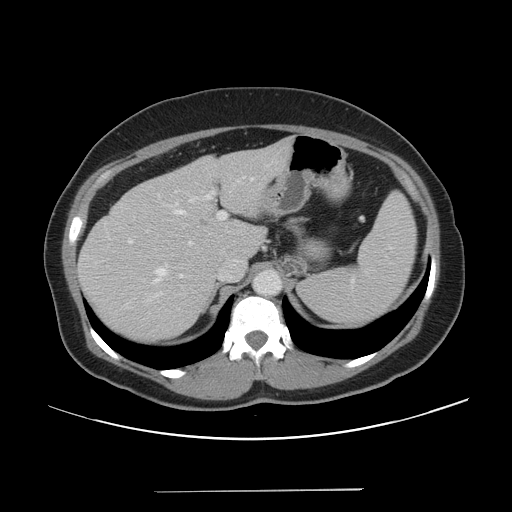
Contrast-enhanced abdominal CT, one axial slice; slice 31 of 56 in the series (ordered by position); 120 kVp; intravenous contrast given; soft-tissue window (W 400 / L 40 HU); 512 × 512 image matrix. Female patient, age 54 years. From the clinical record (not read from this slice): diagnosis: colorectal cancer liver metastases, imaged before liver resection; multiple liver metastases: yes; largest metastasis: 3.2 cm; disease in both lobes: yes.
Structures marked on this image (outlined manually by an expert reader):
- hepatic veins: bounding box (x1, y1, x2, y2) in pixels: (156, 178, 253, 276)
- liver: (78, 139, 294, 343)
- planned liver remnant (the part of the liver to remain after resection): (181, 137, 294, 260)
- portal vein (with intrahepatic branches): (156, 178, 245, 296)